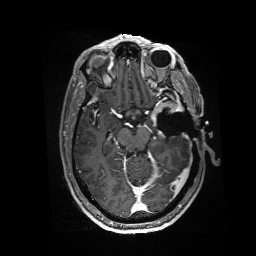
Brain MRI from a brain-tumour surgery series, one axial slice. Slice 99 of 176 in the series (ordered by position). T1-weighted post-contrast. 1 mm slice thickness. 256 × 256 image matrix, field of view 256 × 256 mm. From the clinical record (not read from this slice): histopathology: Glioblastoma; WHO grade: 4; IDH mutation: no.
Annotated regions visible in this slice (manually delineated by an expert):
- residual tumour: bounding box <151,101,185,126> (left, top, right, bottom; pixels)